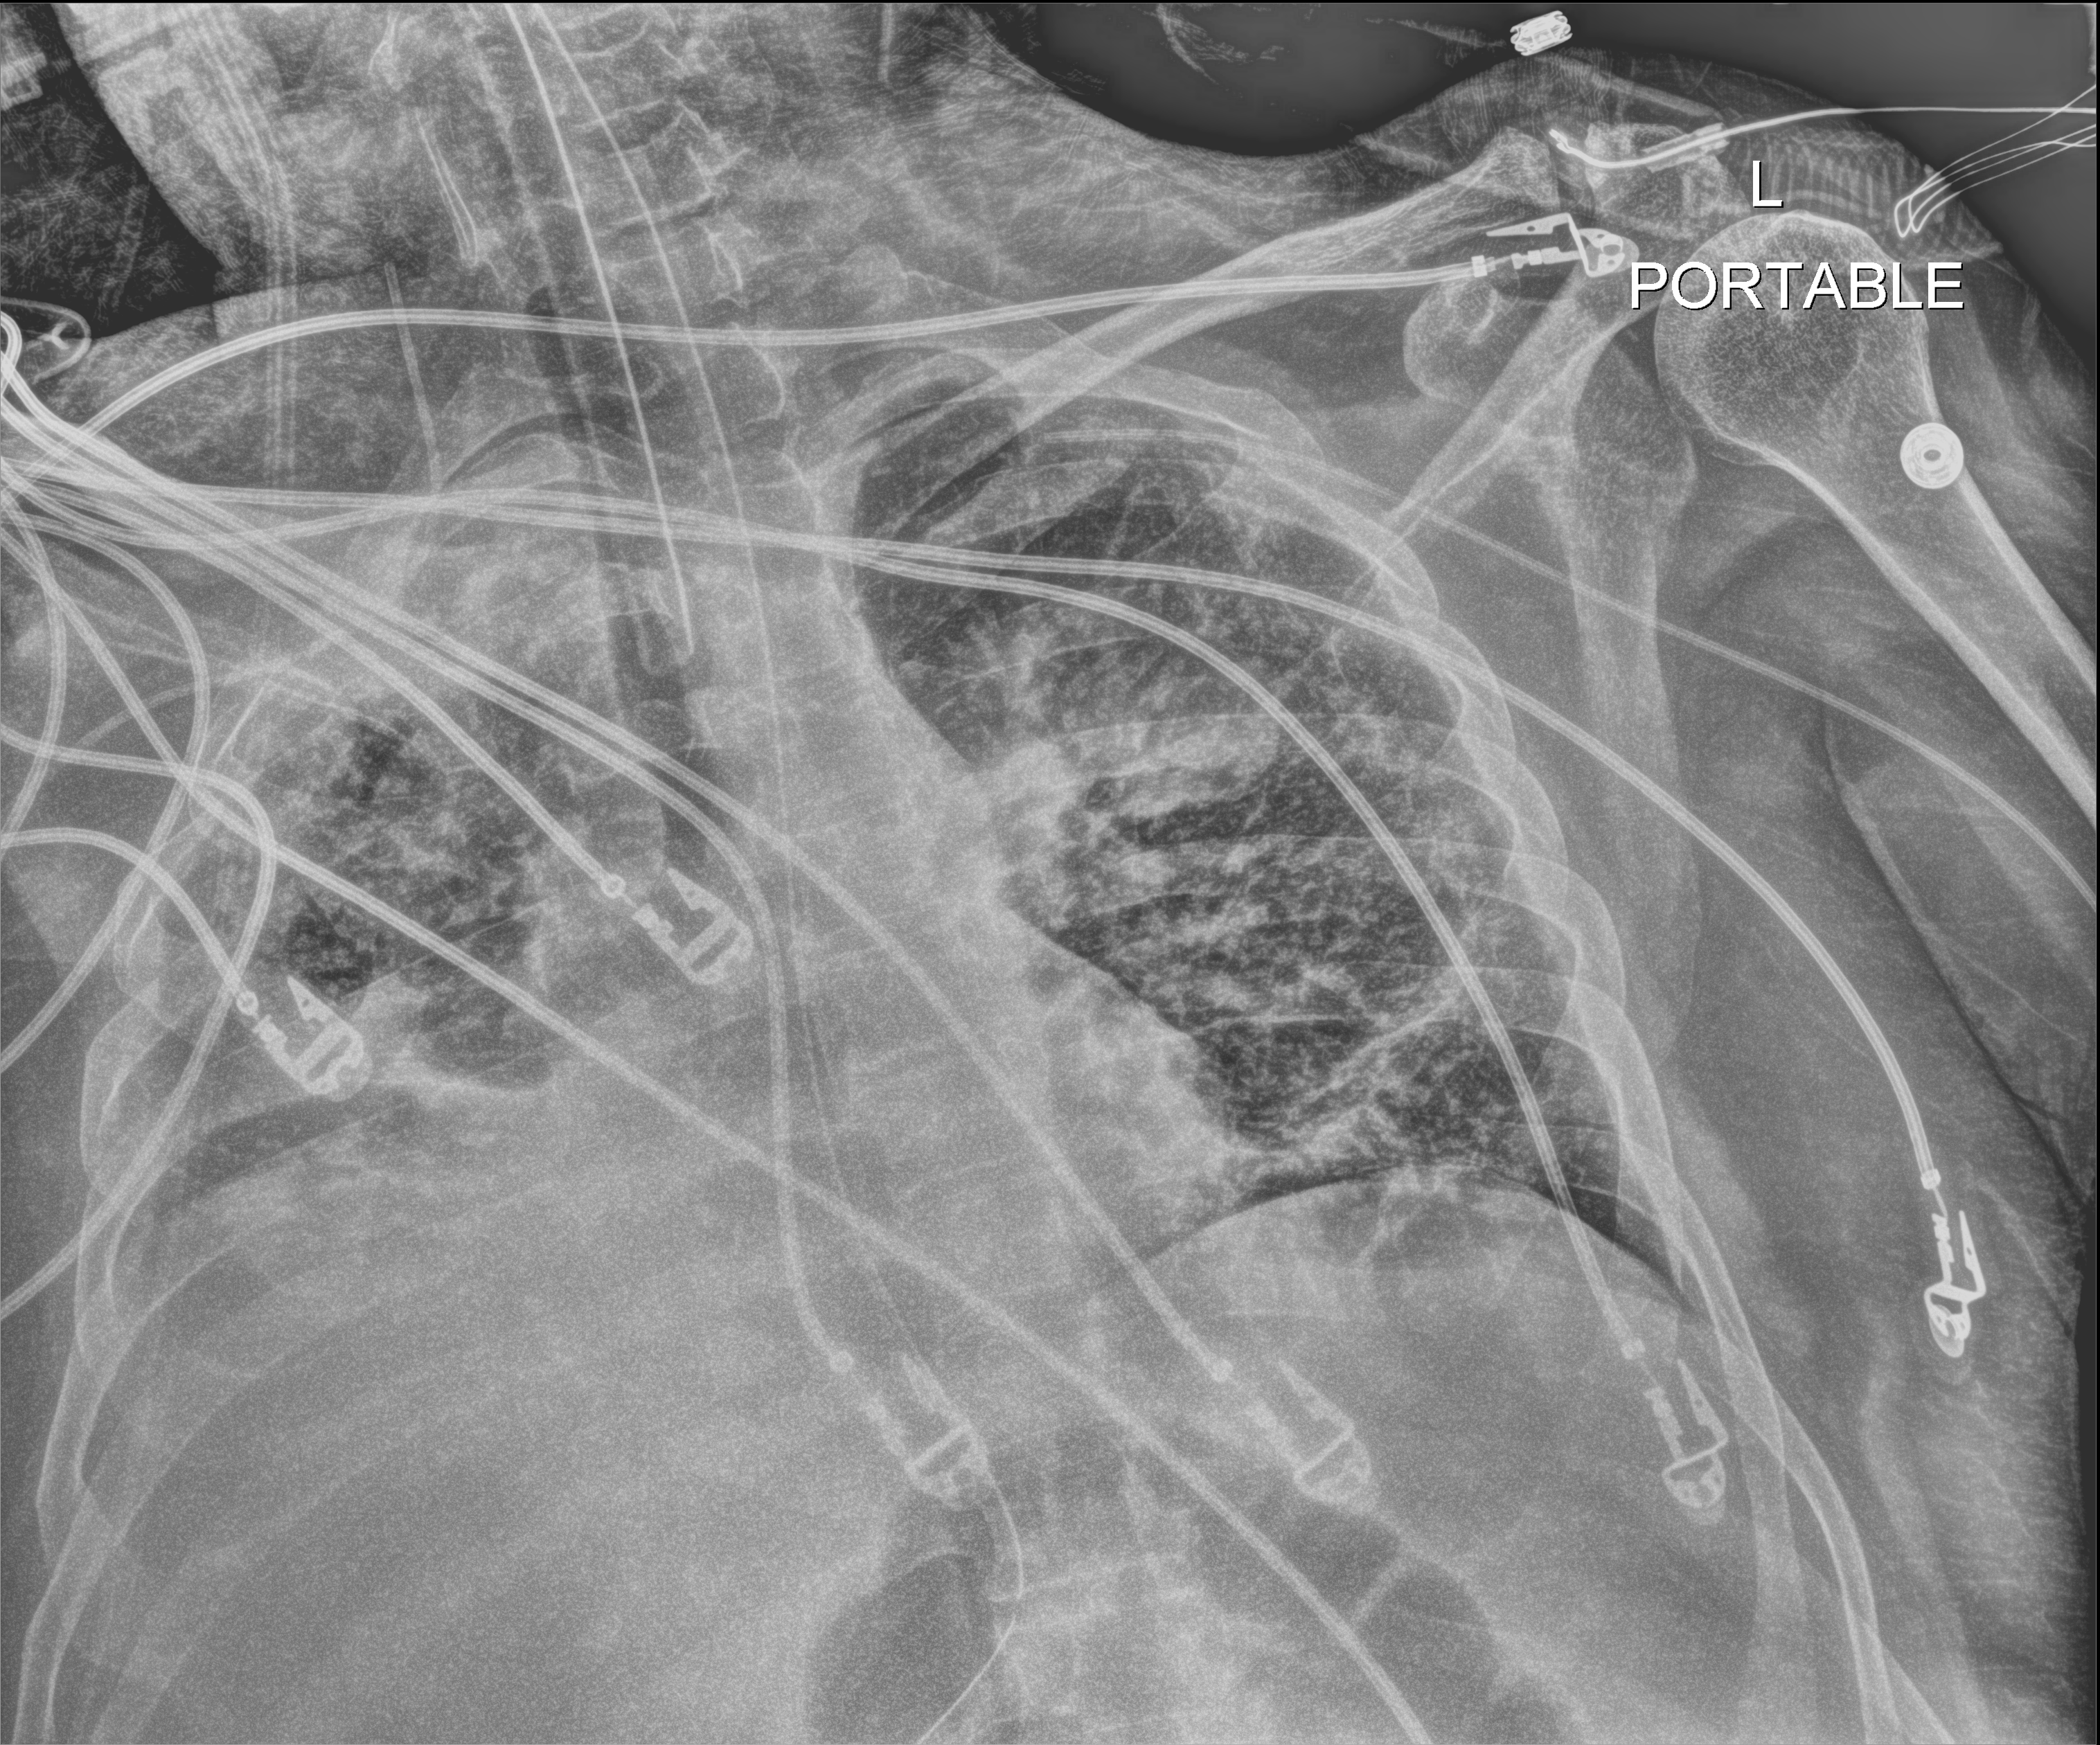
Chest X-ray, anteroposterior (AP) projection. Patient hospitalised with COVID-19, aged 18–59 years.
Hospital-stay facts (about this admission, not read from this image; timing relative to this image not recorded):
- length of hospital stay: 50 days
- mechanically ventilated during this hospital stay: yes